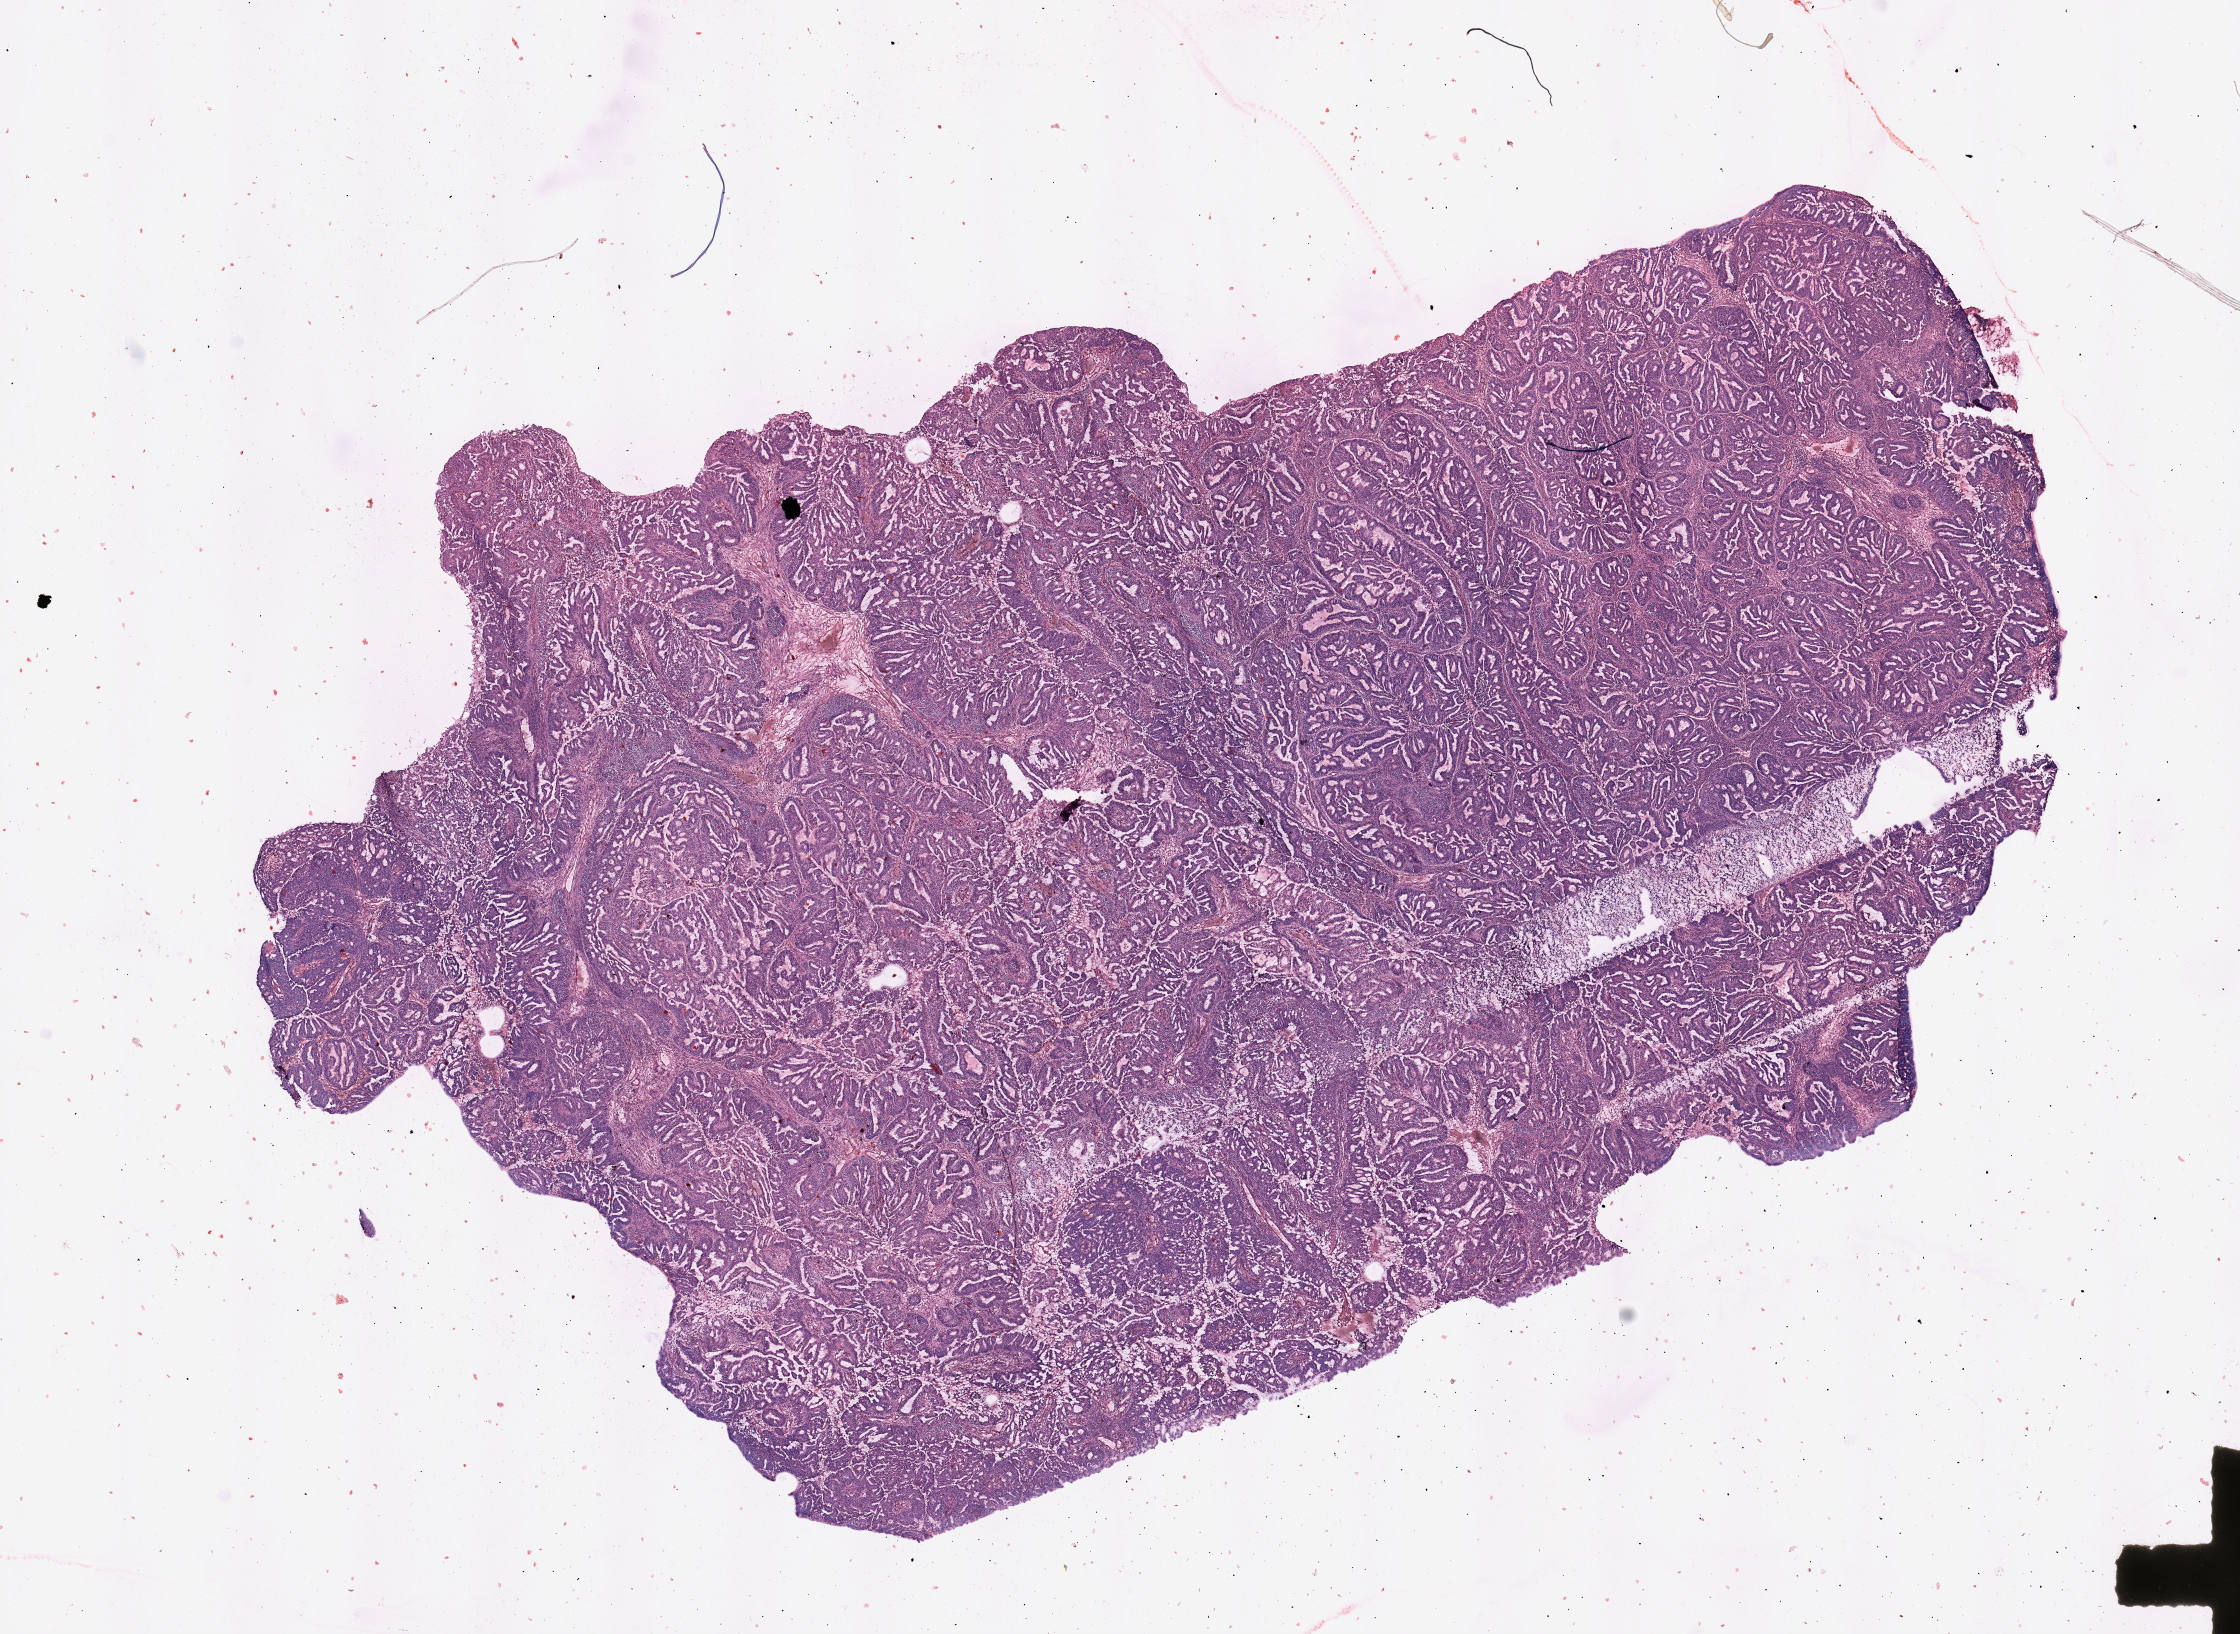
Whole-slide histology image, H&E, low-resolution overview of the scanned area, about 17.7 x 12.9 mm; tumour tissue sample, sampled site: uterus. Female, 59 y/o. Histologic grade: G2 (moderately differentiated). Slide review estimates, as recorded: tumour nuclei 95%, necrosis 0%.
* diagnosis: Endometrioid adenocarcinoma, NOS
* AJCC pathologic stage: I